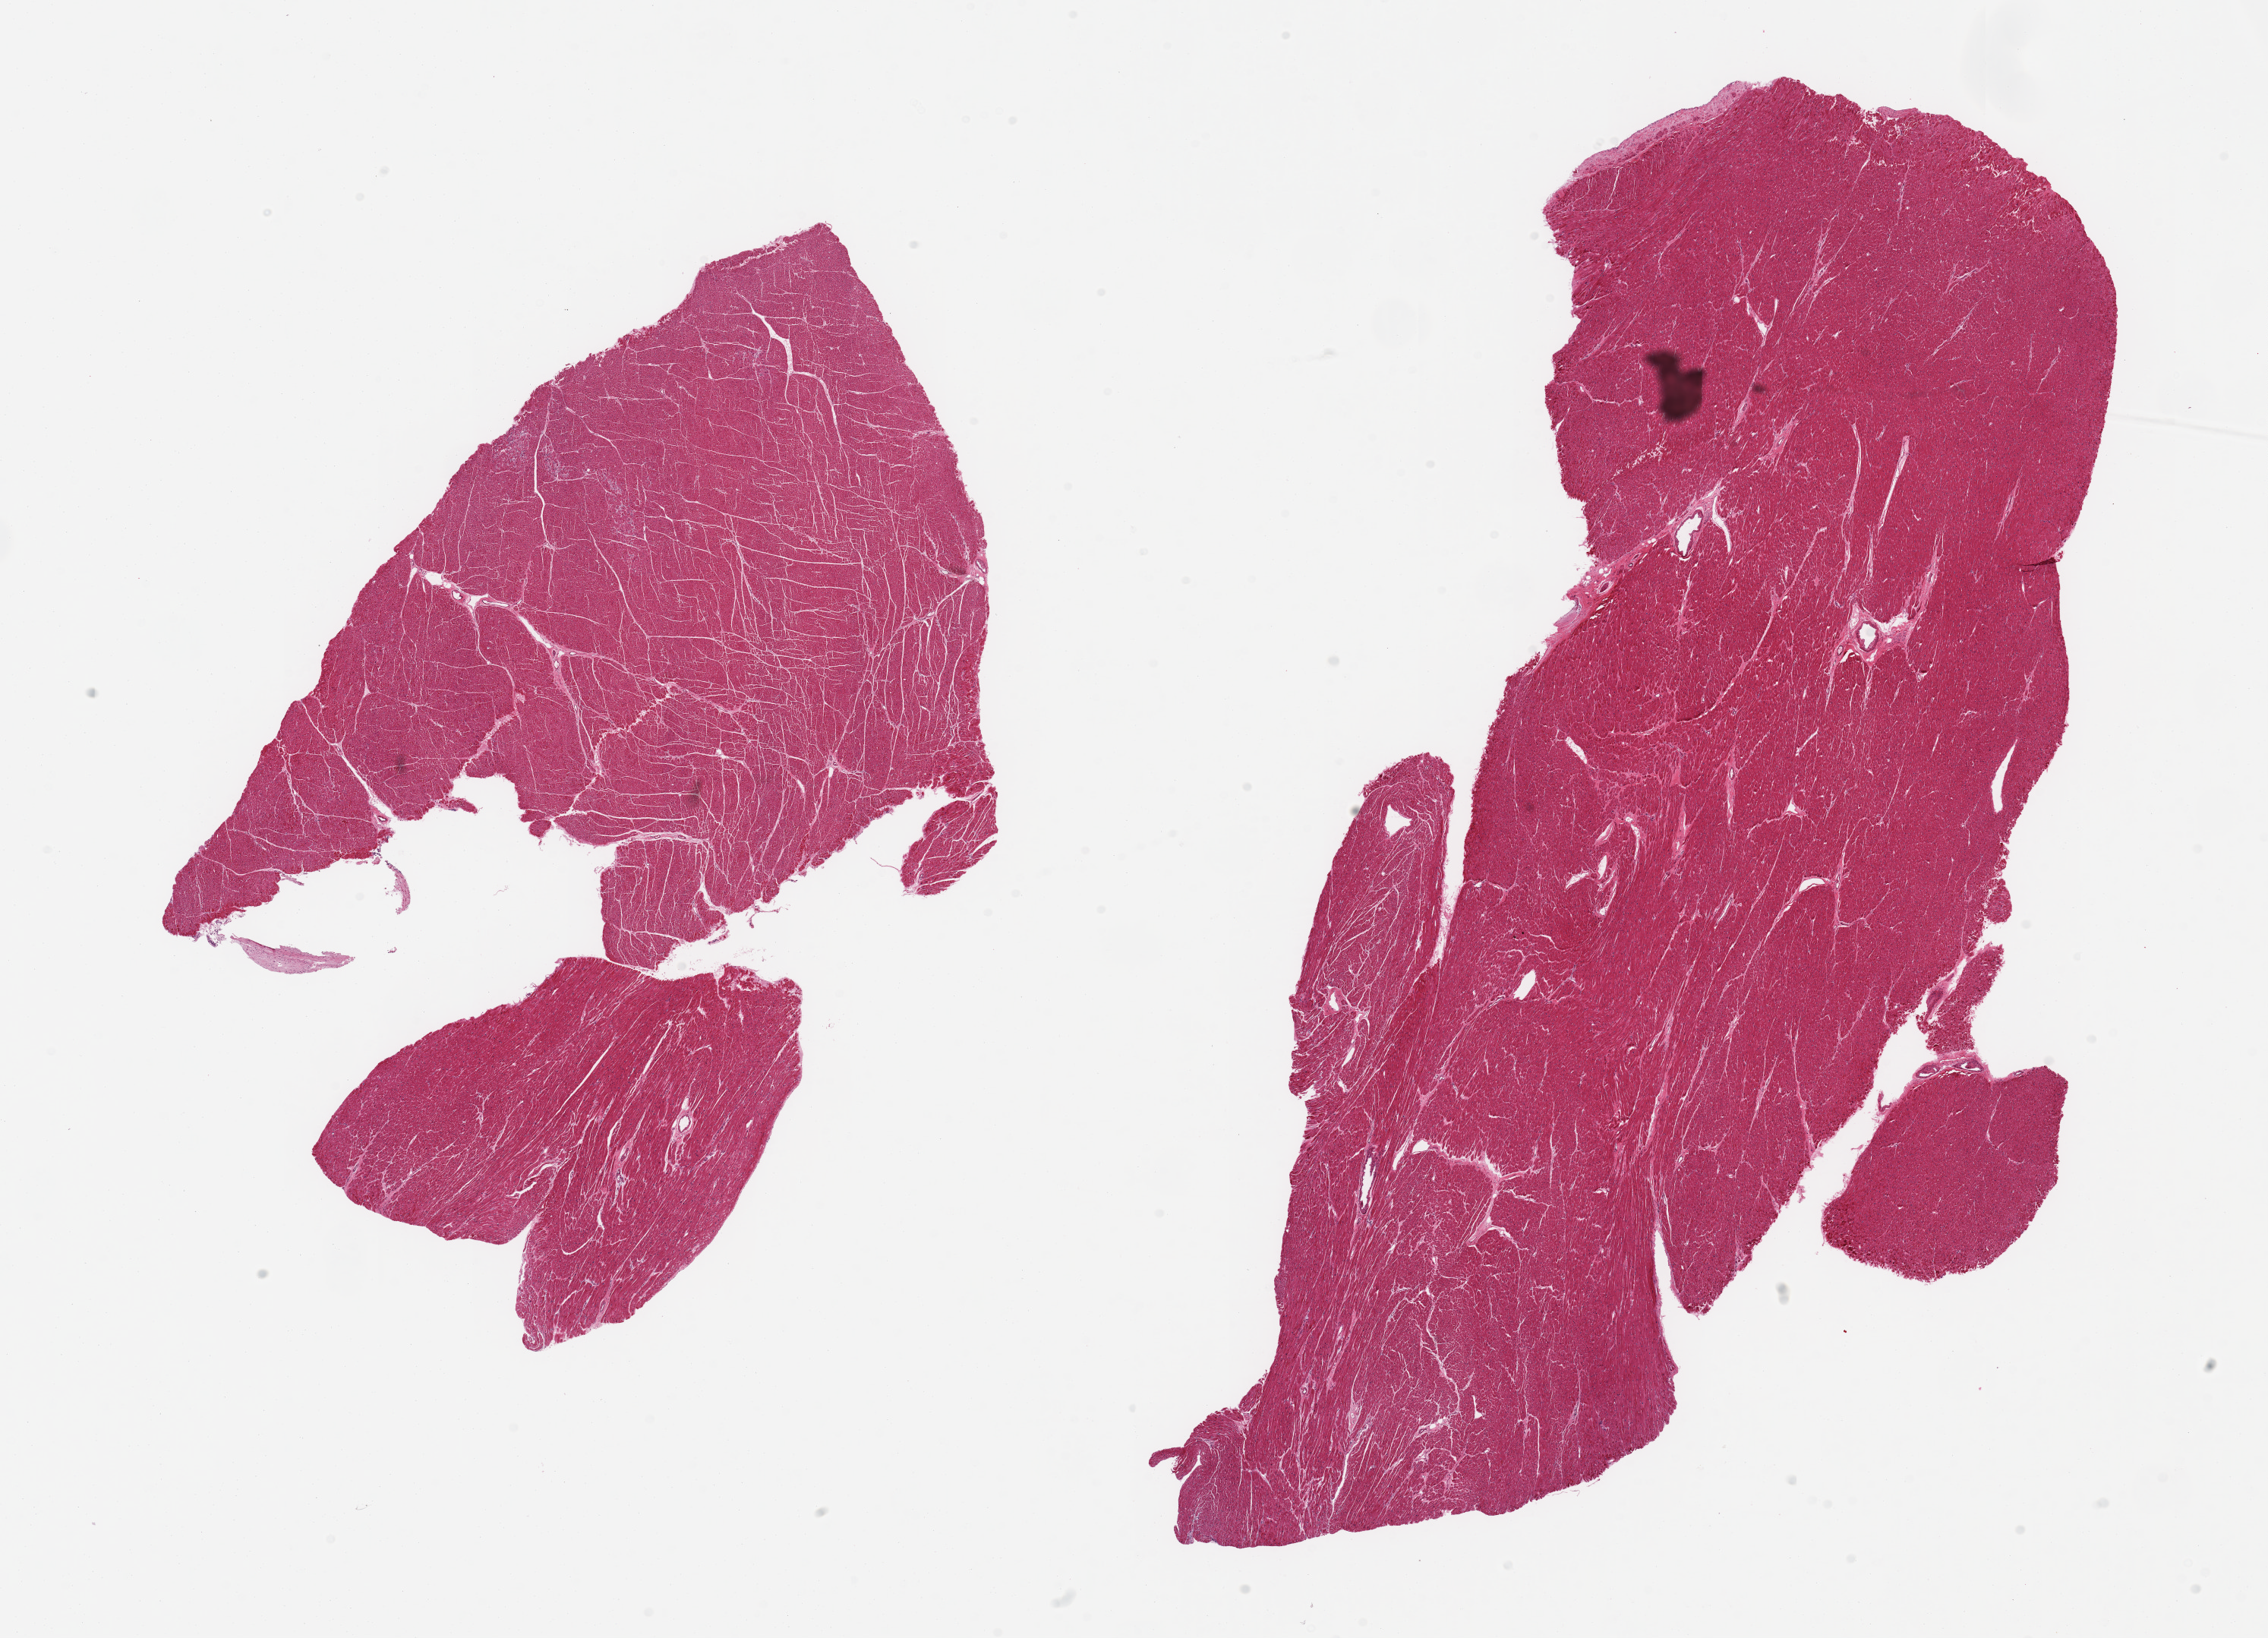
Digitized hematoxylin and eosin (H&E)-stained section — shown as a low-resolution overview of the whole scanned area (about 23.6 x 17.1 mm). PAXgene-fixed, paraffin-embedded tissue. Section of heart (target tissue). Donor tissue sample.
- review note (as recorded): 2 pieces, mild acute ischemic changes (contraction band necrosis)